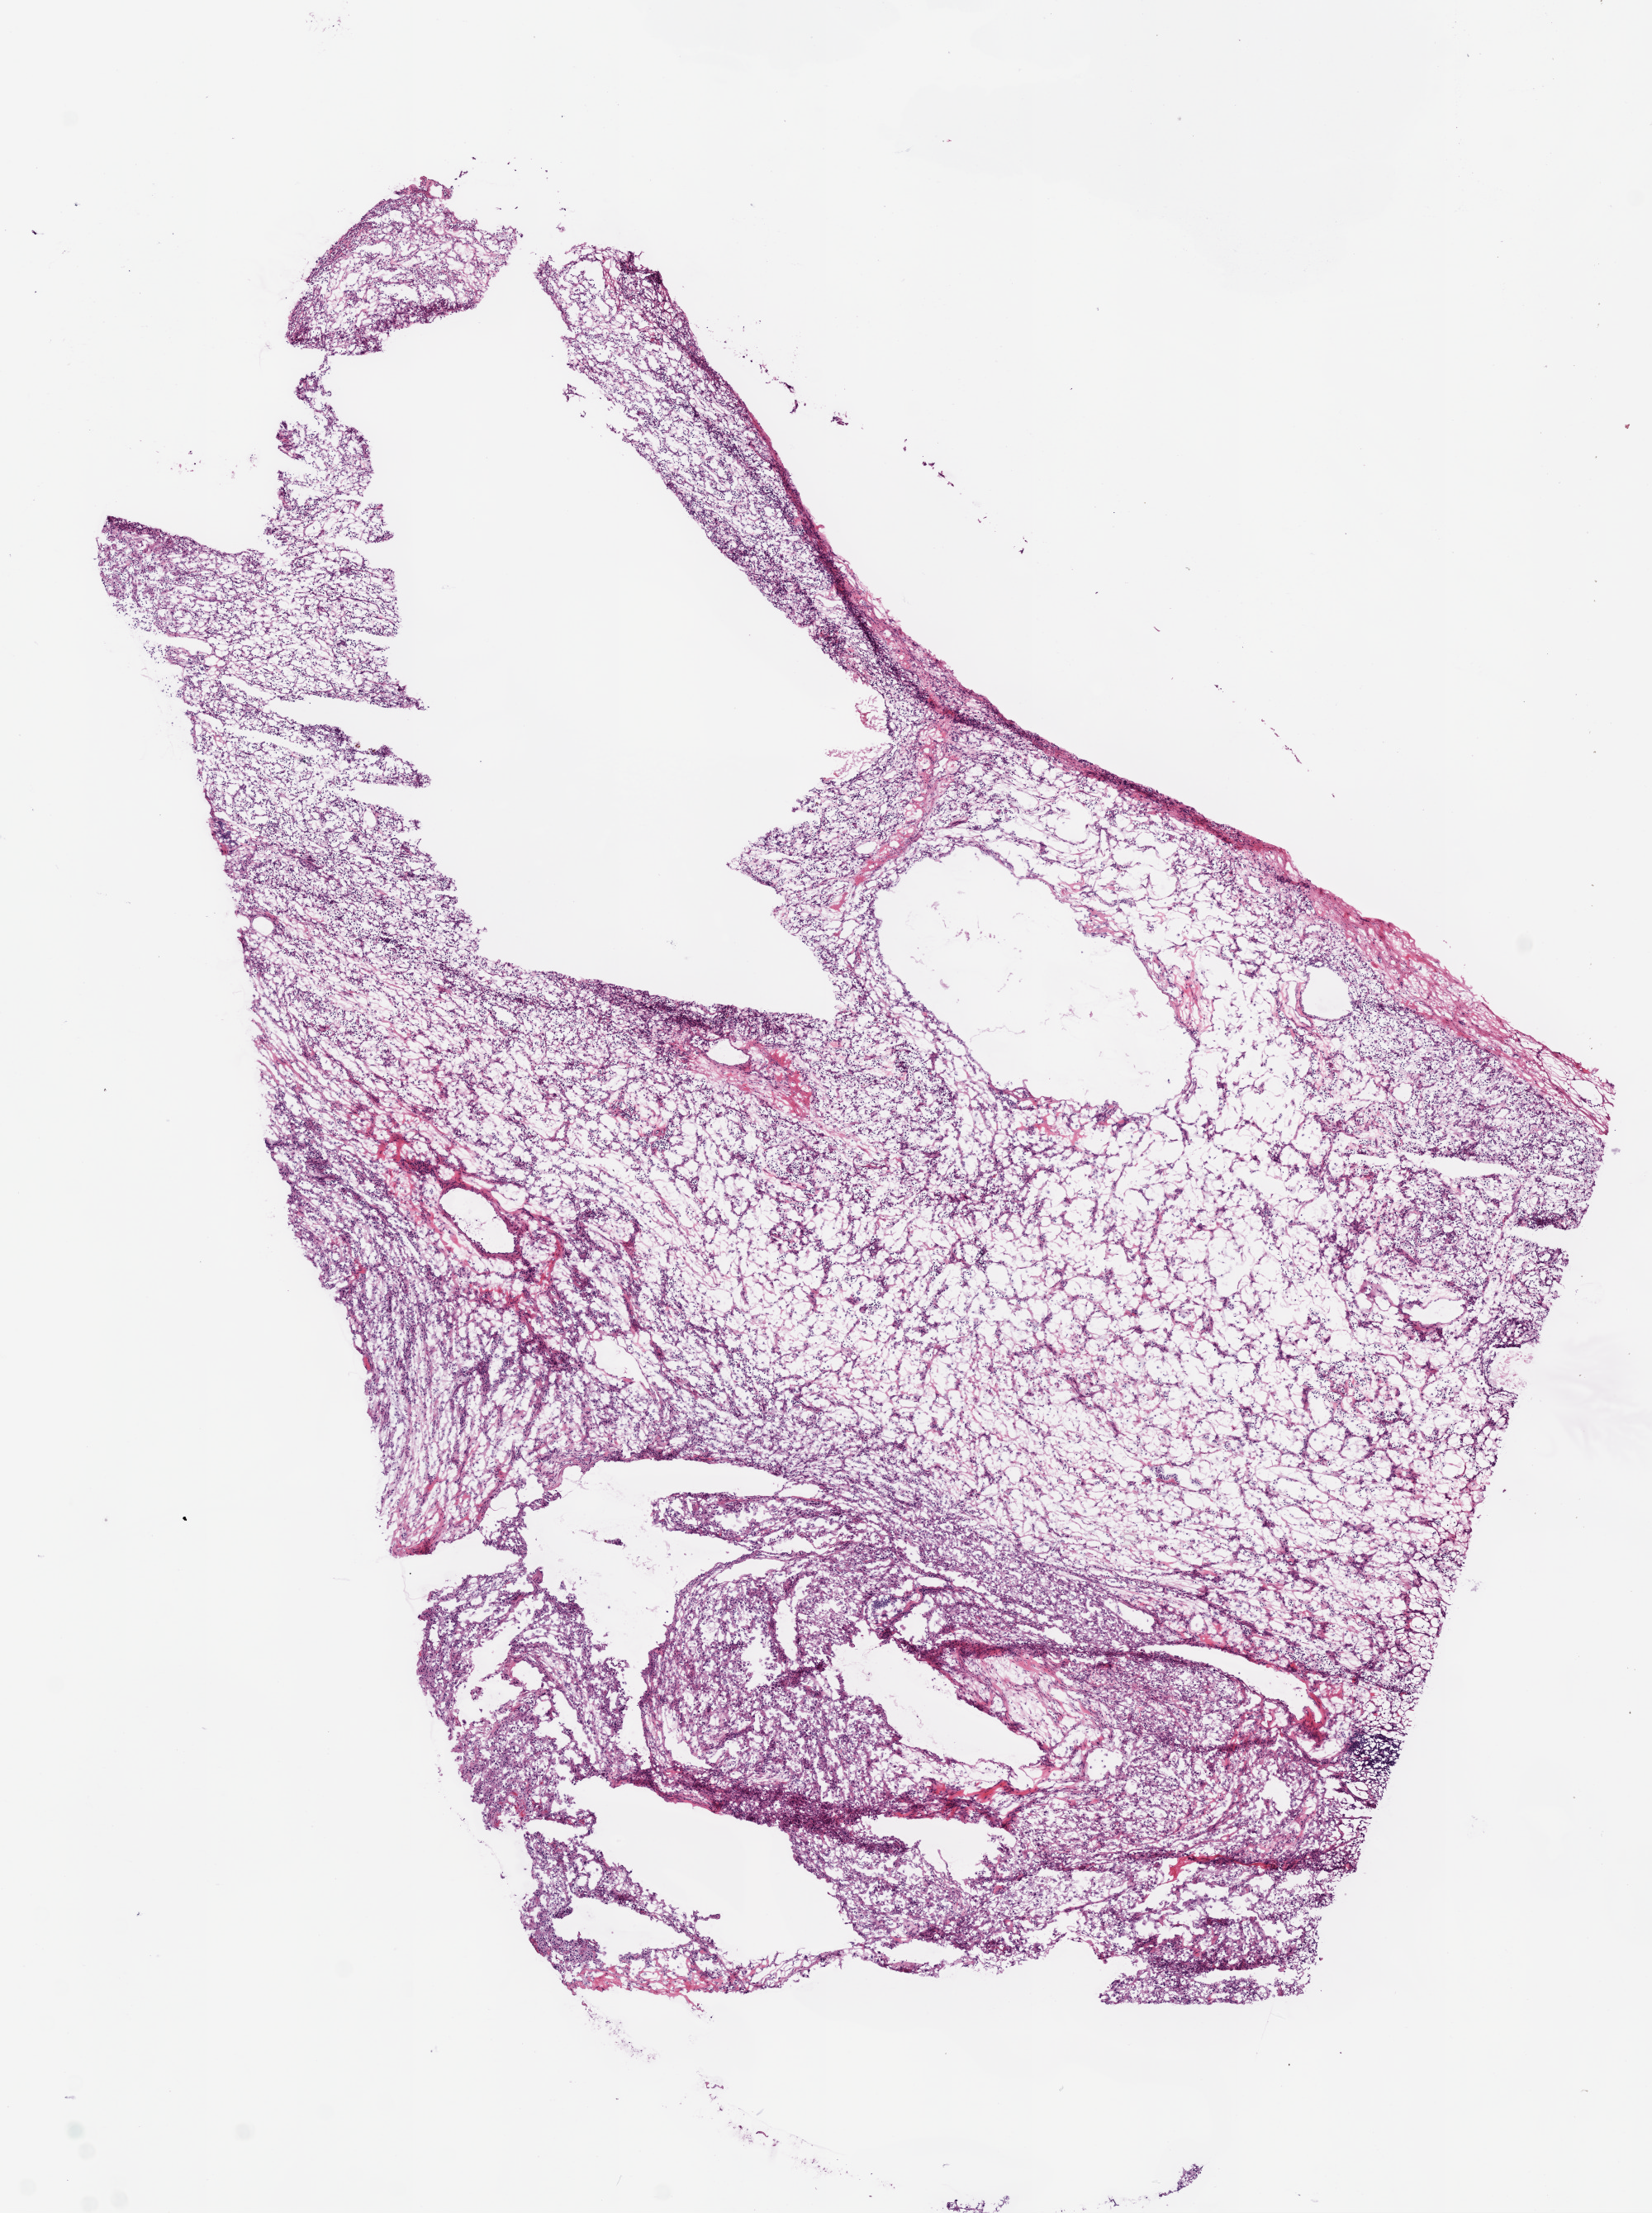
Whole-slide histology image, H&E-stained, whole scanned area (about 8.0 x 10.7 mm, slide scanned at 20x) shown as a low-resolution overview, frozen section from the bottom of the tissue portion, primary tumour sample from the kidney. Patient: female, age at initial diagnosis 62 years. Histologic grade: G3 (poorly differentiated). Slide review estimates, as recorded: tumour cells 90%, tumour nuclei 80%, normal cells 0%, stromal cells 10%, necrosis 0%.
Laterality: right. Histologic diagnosis: Clear cell adenocarcinoma, NOS. TNM: T2 NX M0. AJCC pathologic stage: II.